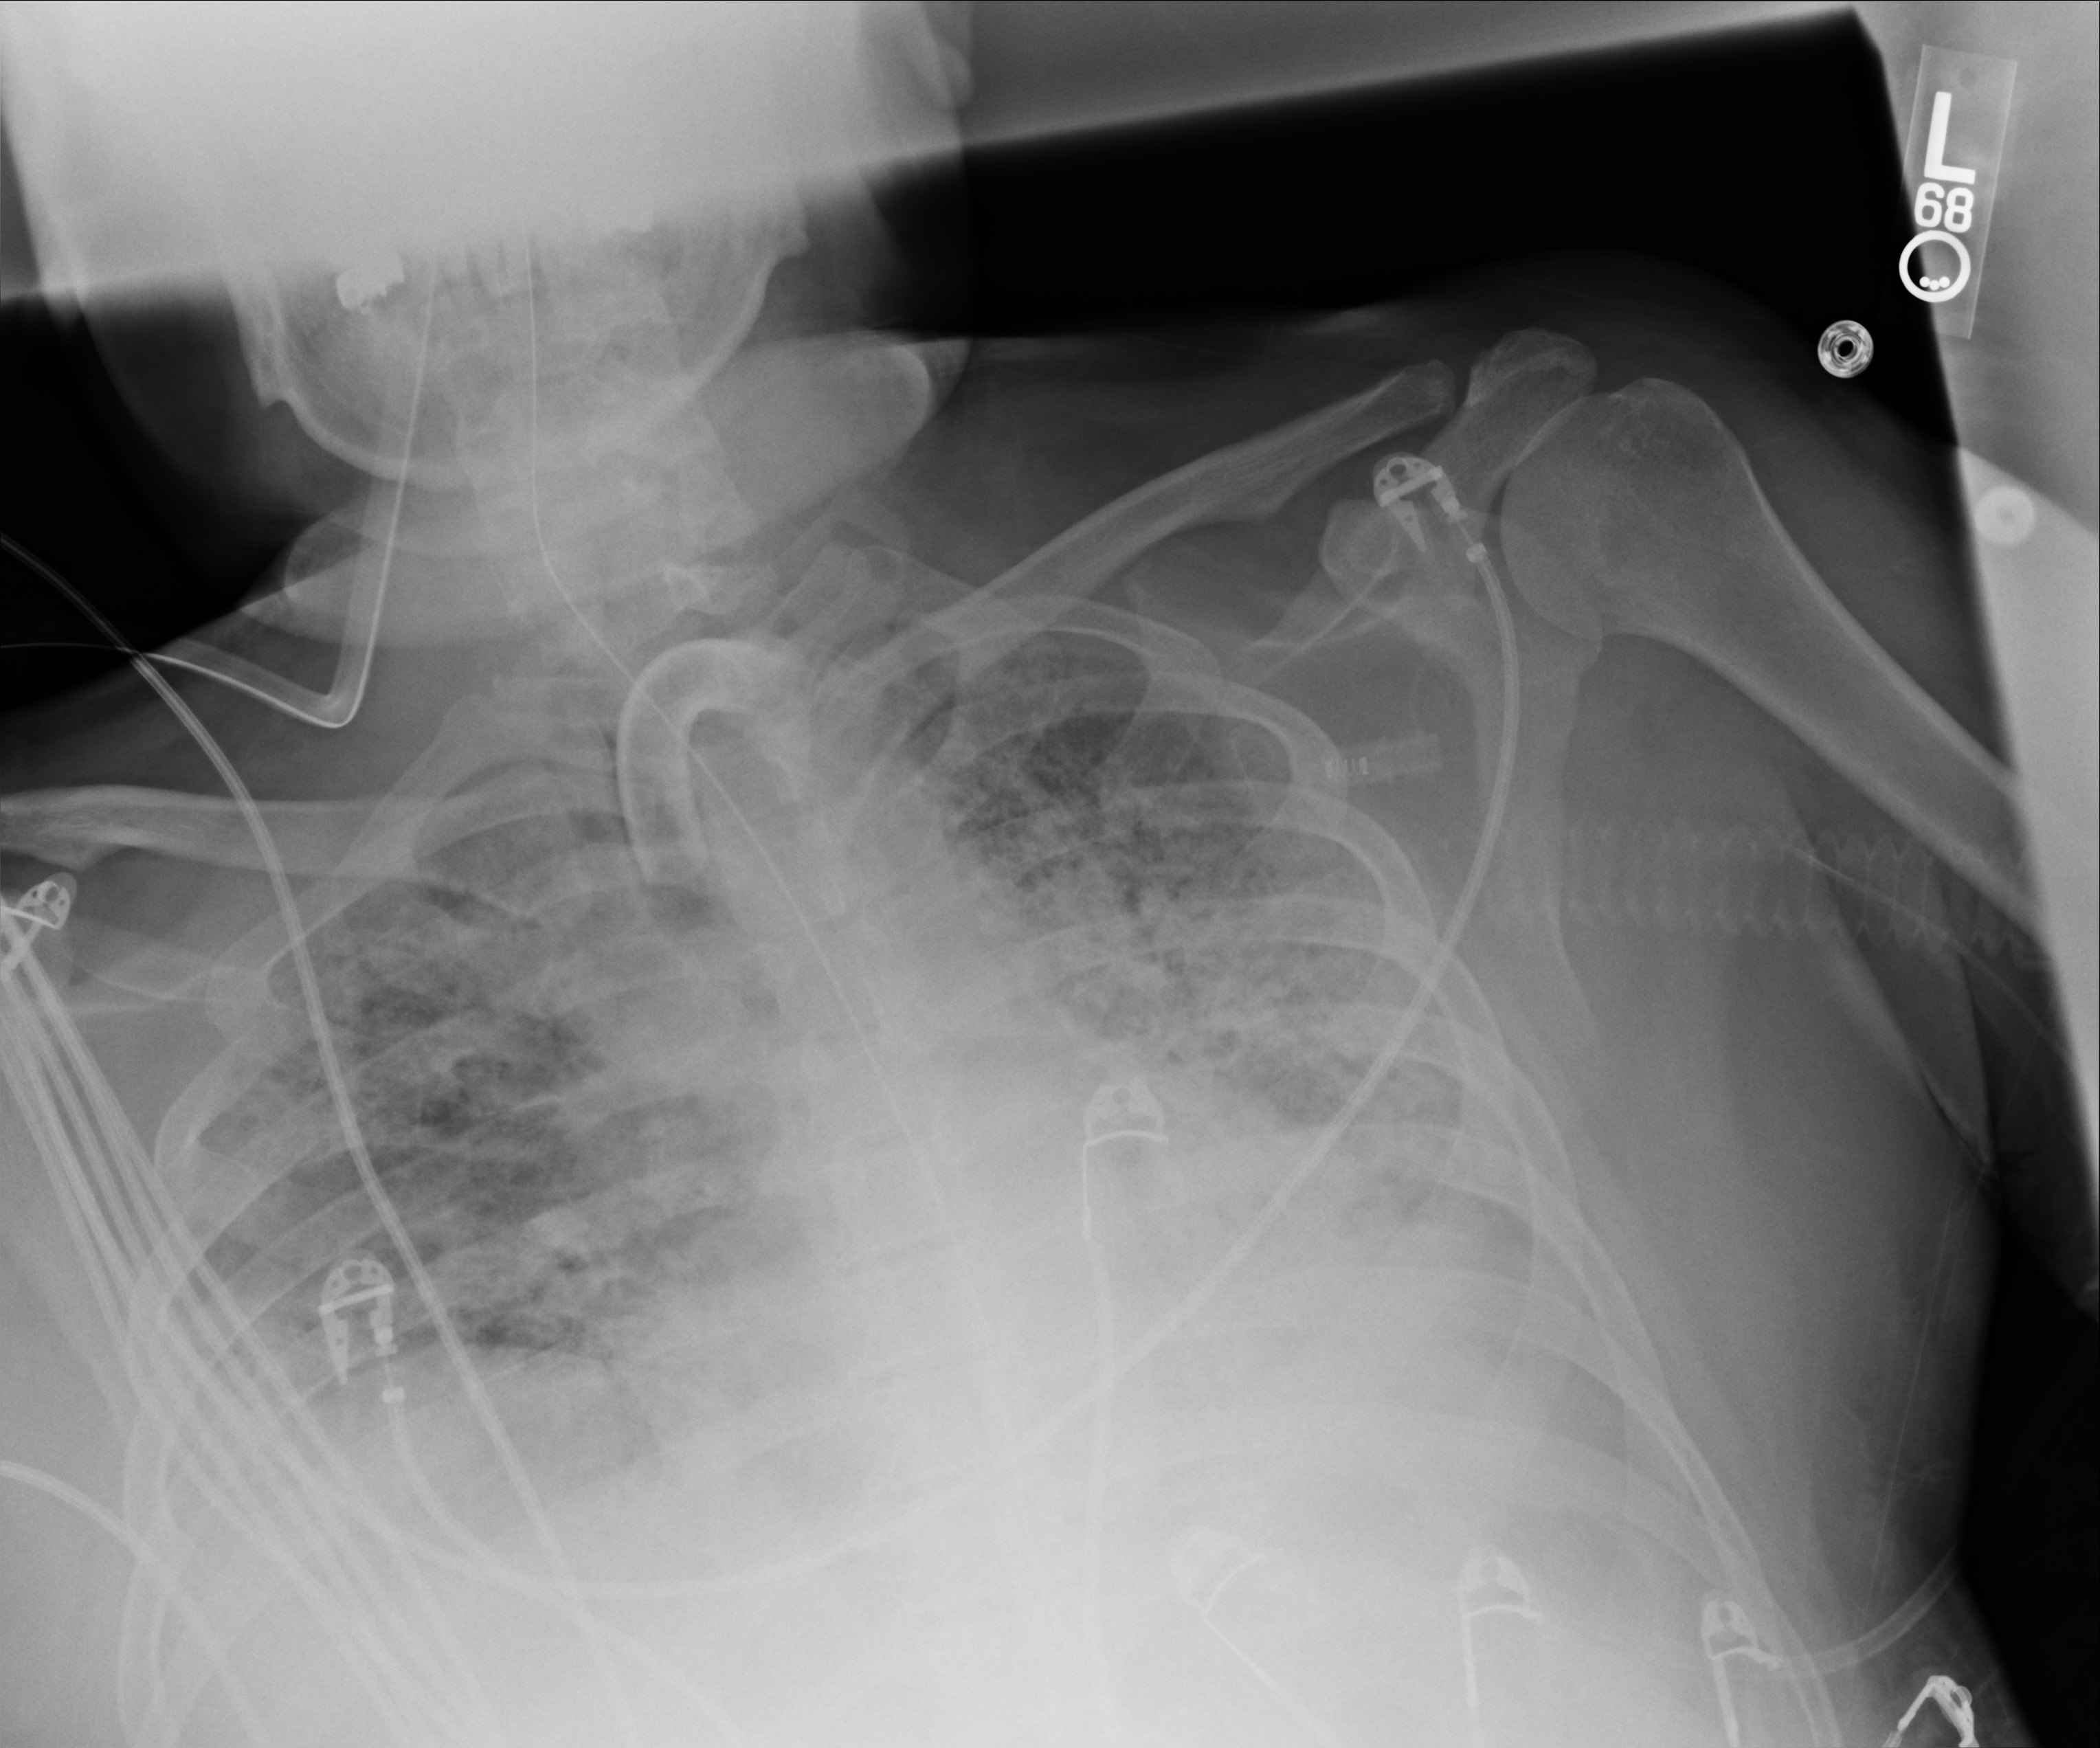
Portable chest radiograph; anteroposterior (AP) projection. Patient hospitalised with COVID-19; male, aged 18–59 years.
Admission-level facts for this patient (not findings on this image; timing relative to this image not recorded):
- mechanically ventilated during this hospital stay: yes
- smoking status (admission record): never